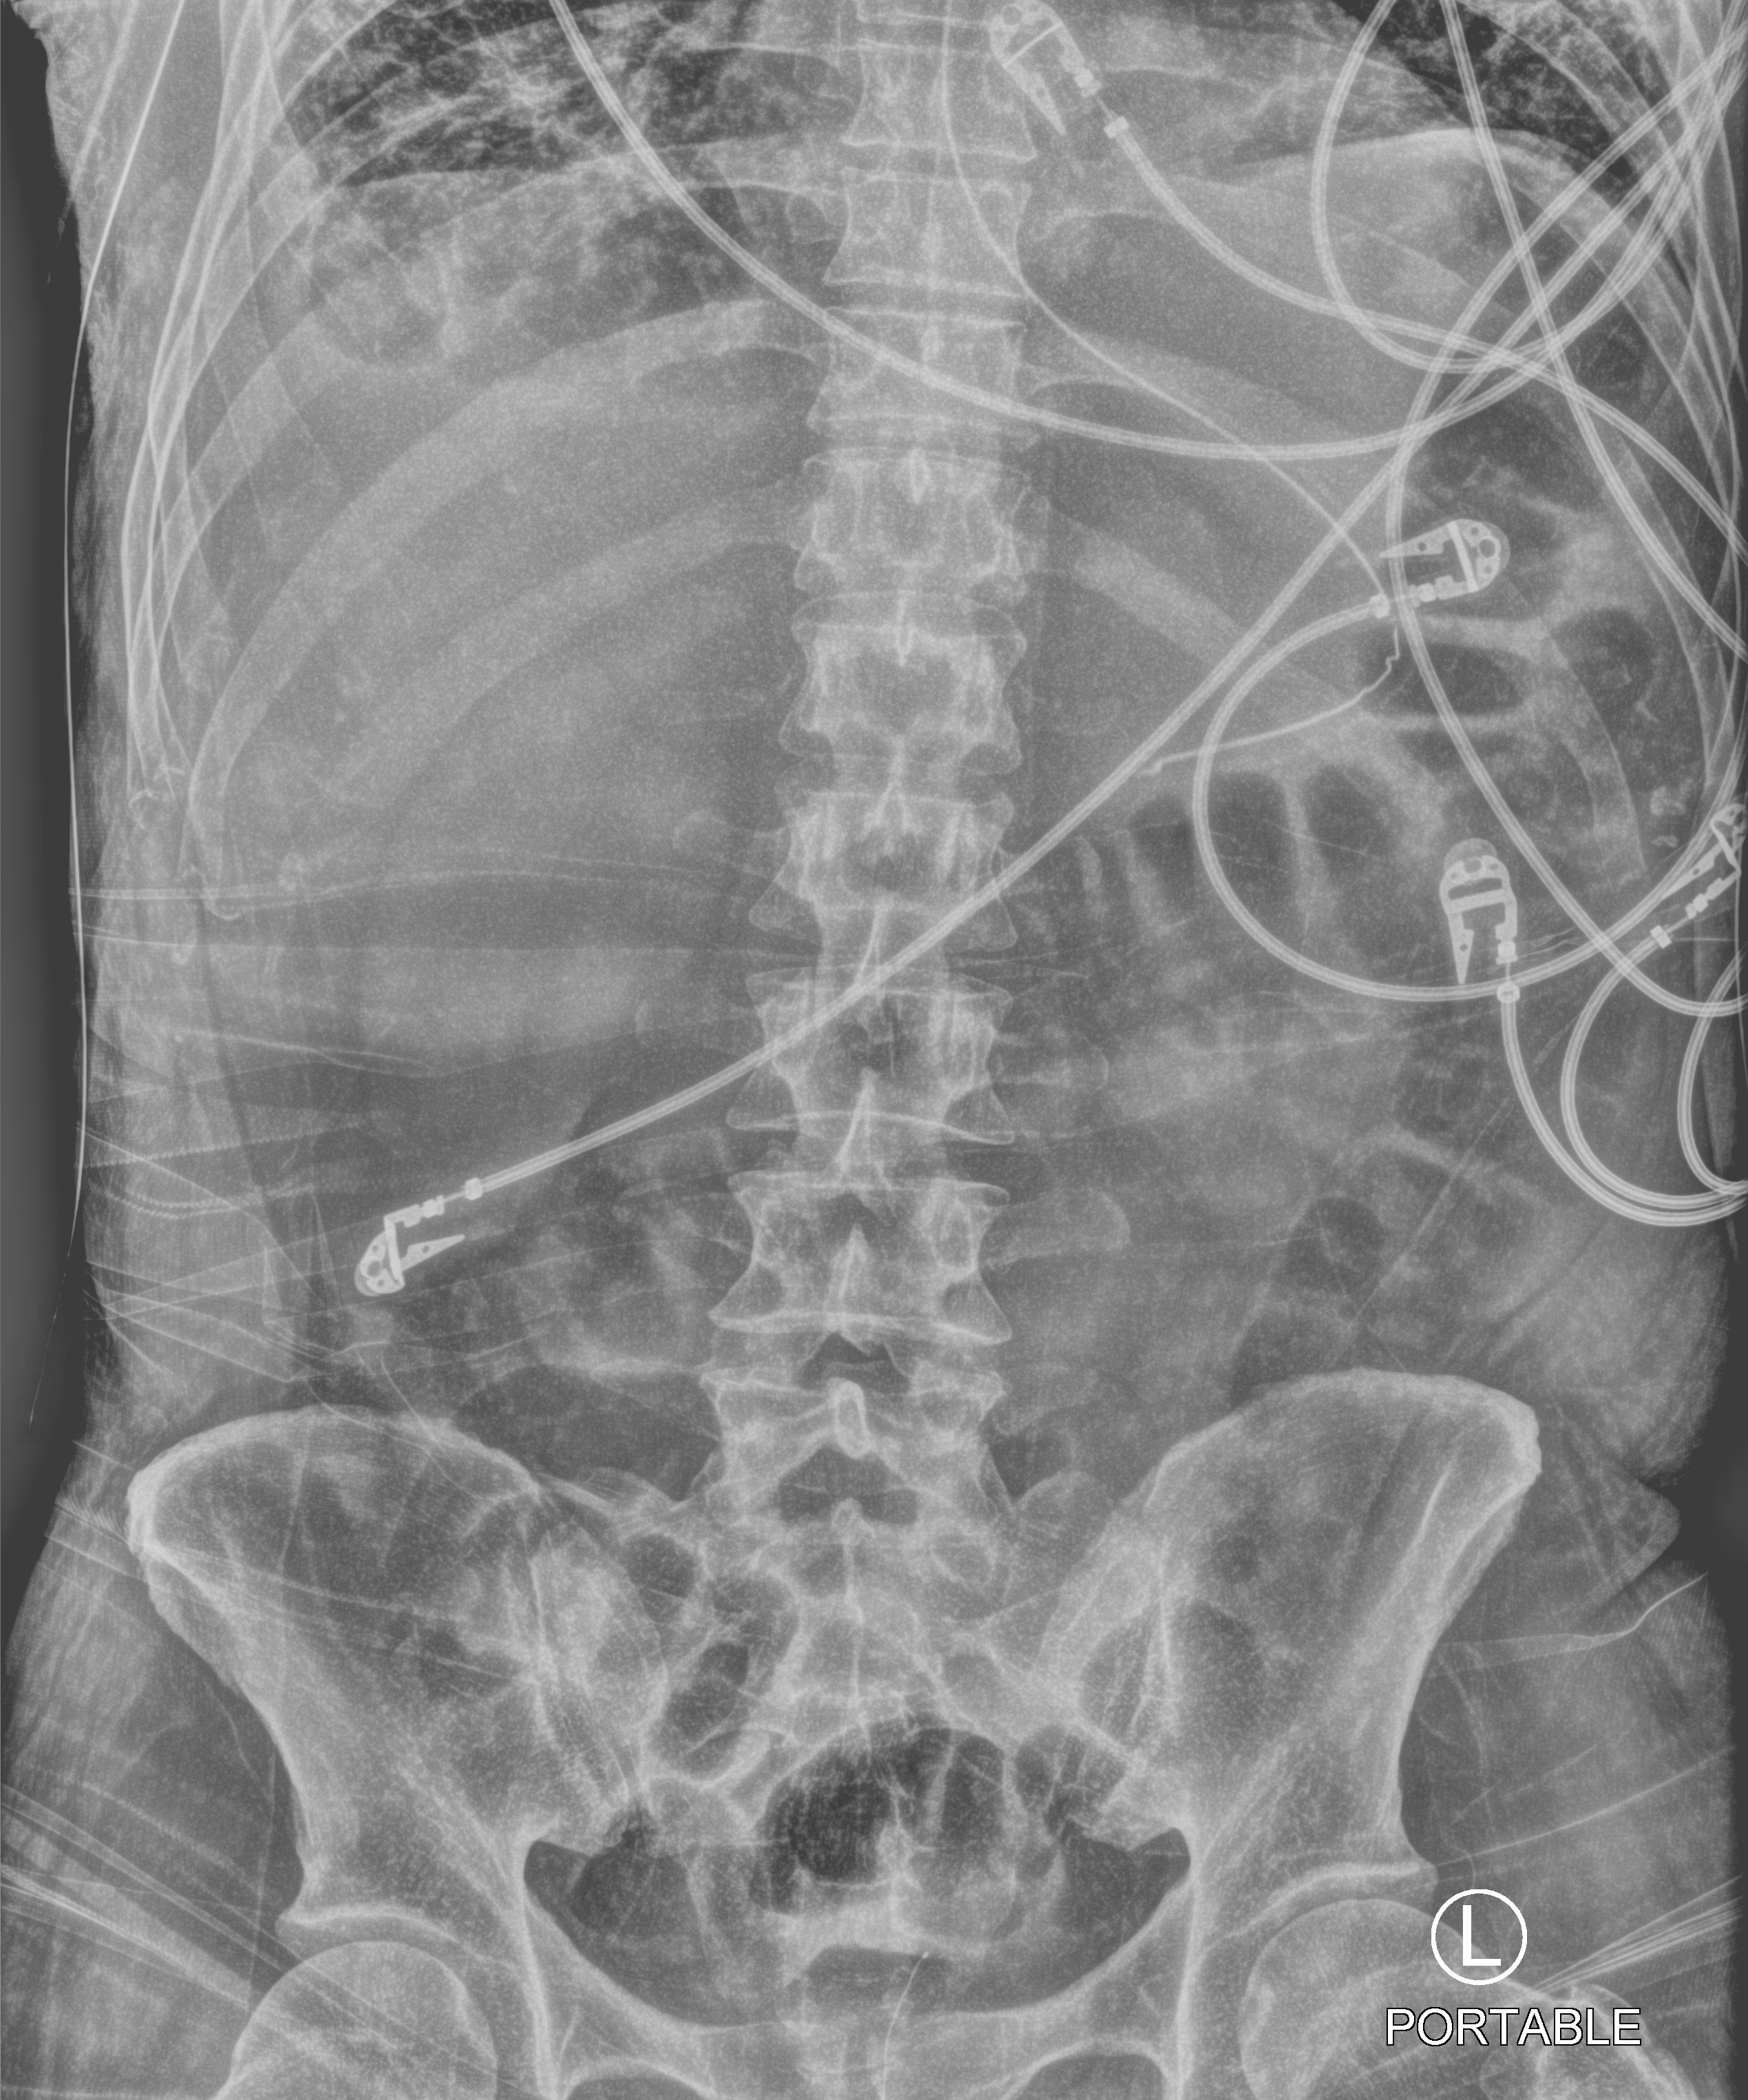
Portable abdomen radiograph; anteroposterior (AP) projection. Male patient hospitalised with COVID-19, age 18–59 years.
From the hospital-stay record, not from the radiograph (when in the stay this image was taken is not recorded): smoking status (admission record): never.